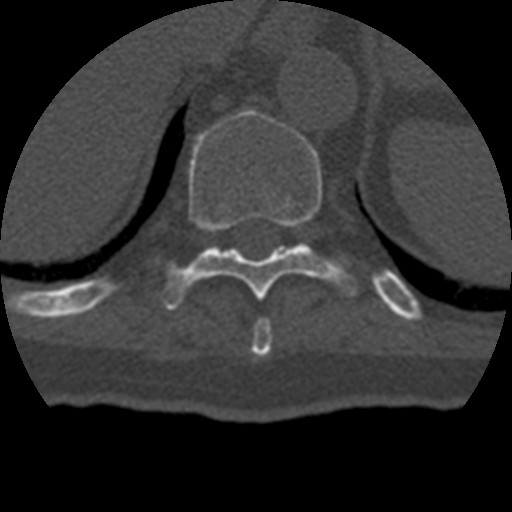
CT including the spine, one axial slice; position 217 of 399 along the scan axis; 120 kVp; bone window (W 1800 / L 400 HU); 1.25 mm slice thickness; 512 × 512 image matrix, field of view 160 × 160 mm. Patient age 69 years. From the clinical record (not read from this slice): primary cancer: prostate.
Outlined on this slice (semi-automatically segmented with operator editing):
- T10 vertebra: bounding box [x1, y1, x2, y2] px = [162, 109, 358, 311]
- T9 vertebra: [252, 318, 273, 357]